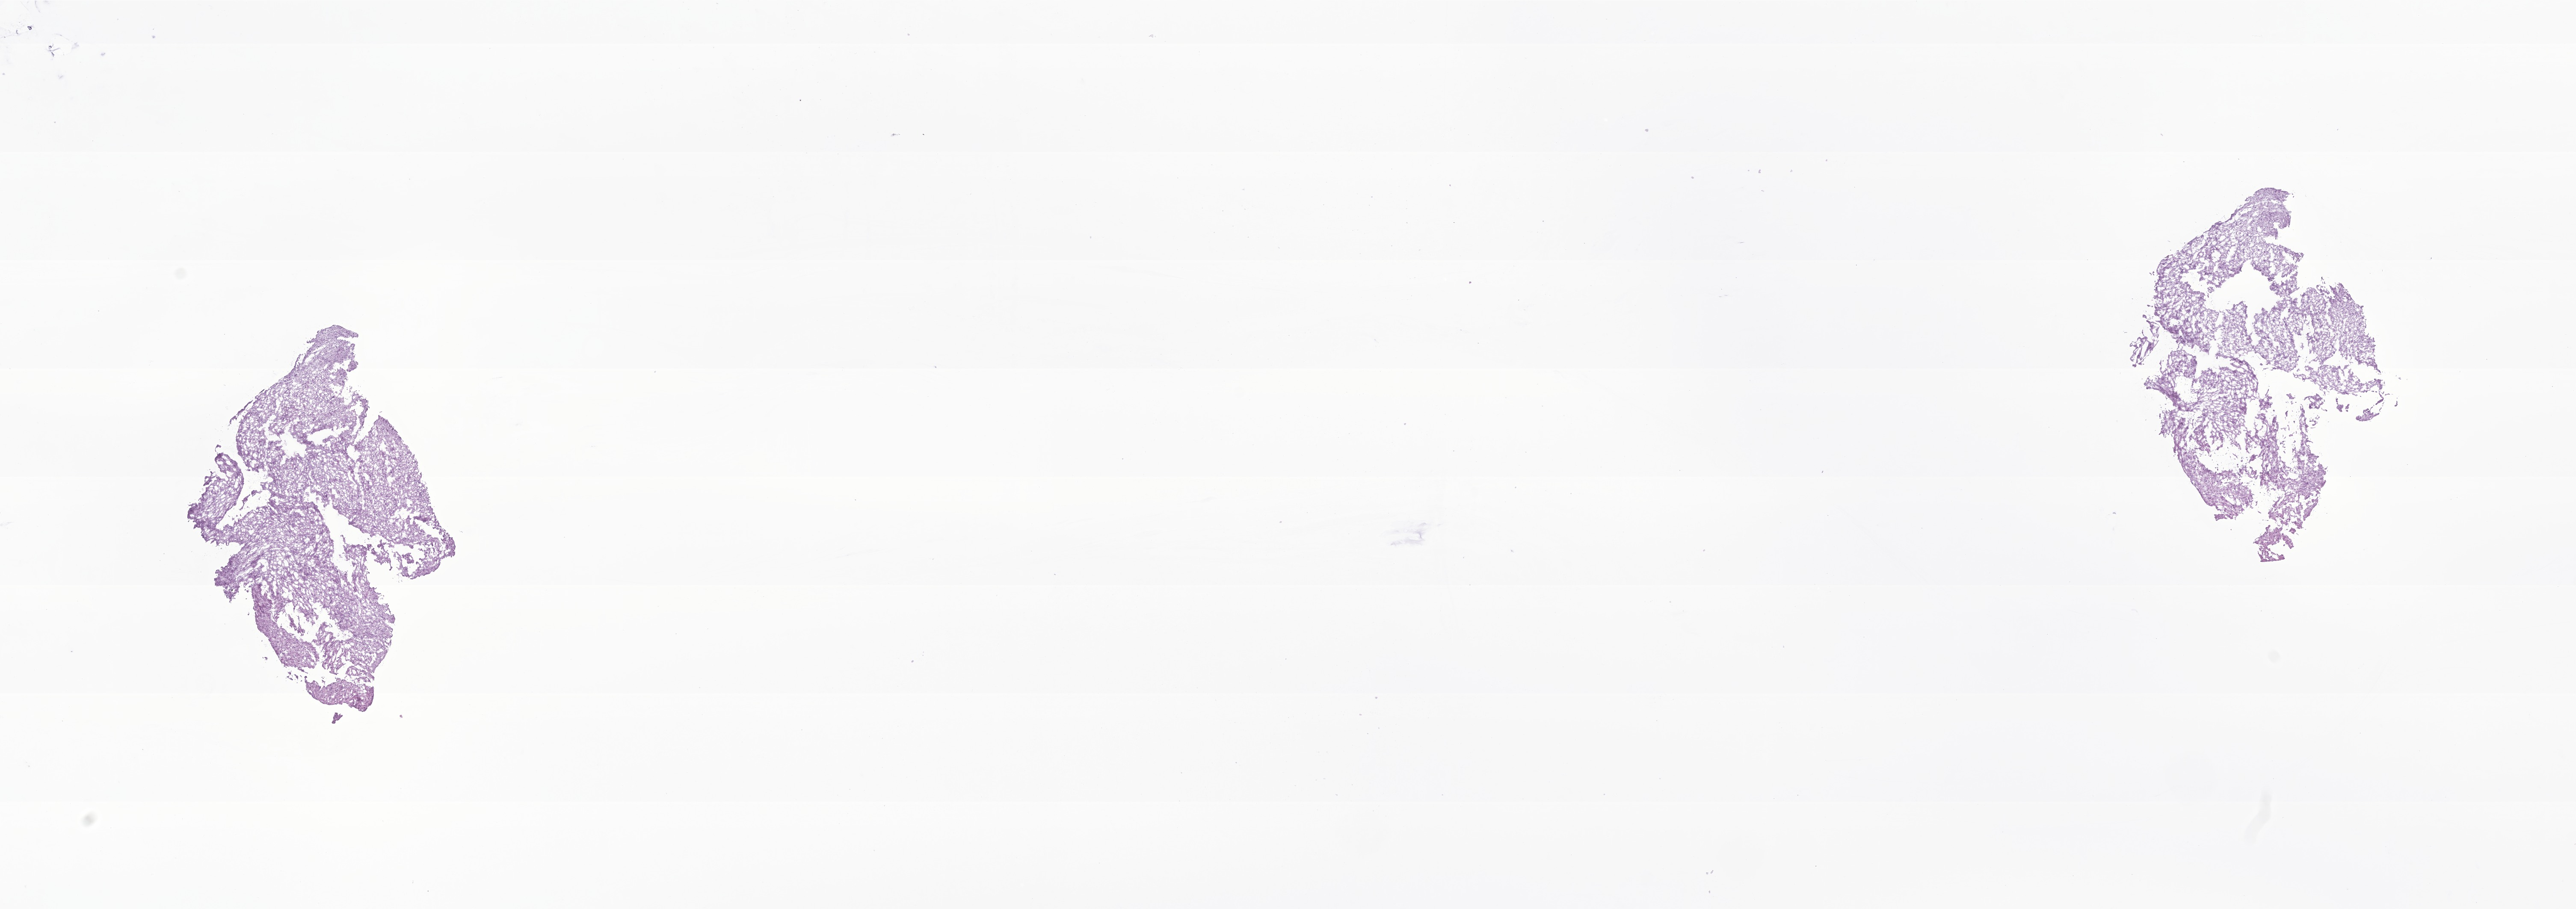
Digitized hematoxylin and eosin (H&E)-stained section of tumor tissue from the head and neck — whole scanned area (about 25.4 x 9.0 mm) shown as a low-resolution overview. Frozen section (OCT-embedded). Patient male; age 132 months (11 years).
* diagnosis (ICD-O-3 morphology term): Neoplasm, uncertain whether benign or malignant